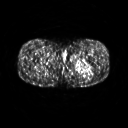
FDG PET of an extremity soft-tissue mass (from a PET/CT study), one axial slice. Slice 244 of 267 in the series (ordered by position). 3.27 mm slice thickness. 128 × 128 image matrix, field of view 500 × 500 mm. Patient: male, 27 years. Case-level facts recorded for this patient, not image findings: histological type: extraskeletal osteosarcoma; grade: high; site of the primary tumour: left adductur.
Outlined on this slice (expert contour drawn on MRI and transferred to this co-registered scan by the dataset authors):
- gross tumour volume (mass): box from (x=71, y=59) to (x=95, y=75) px